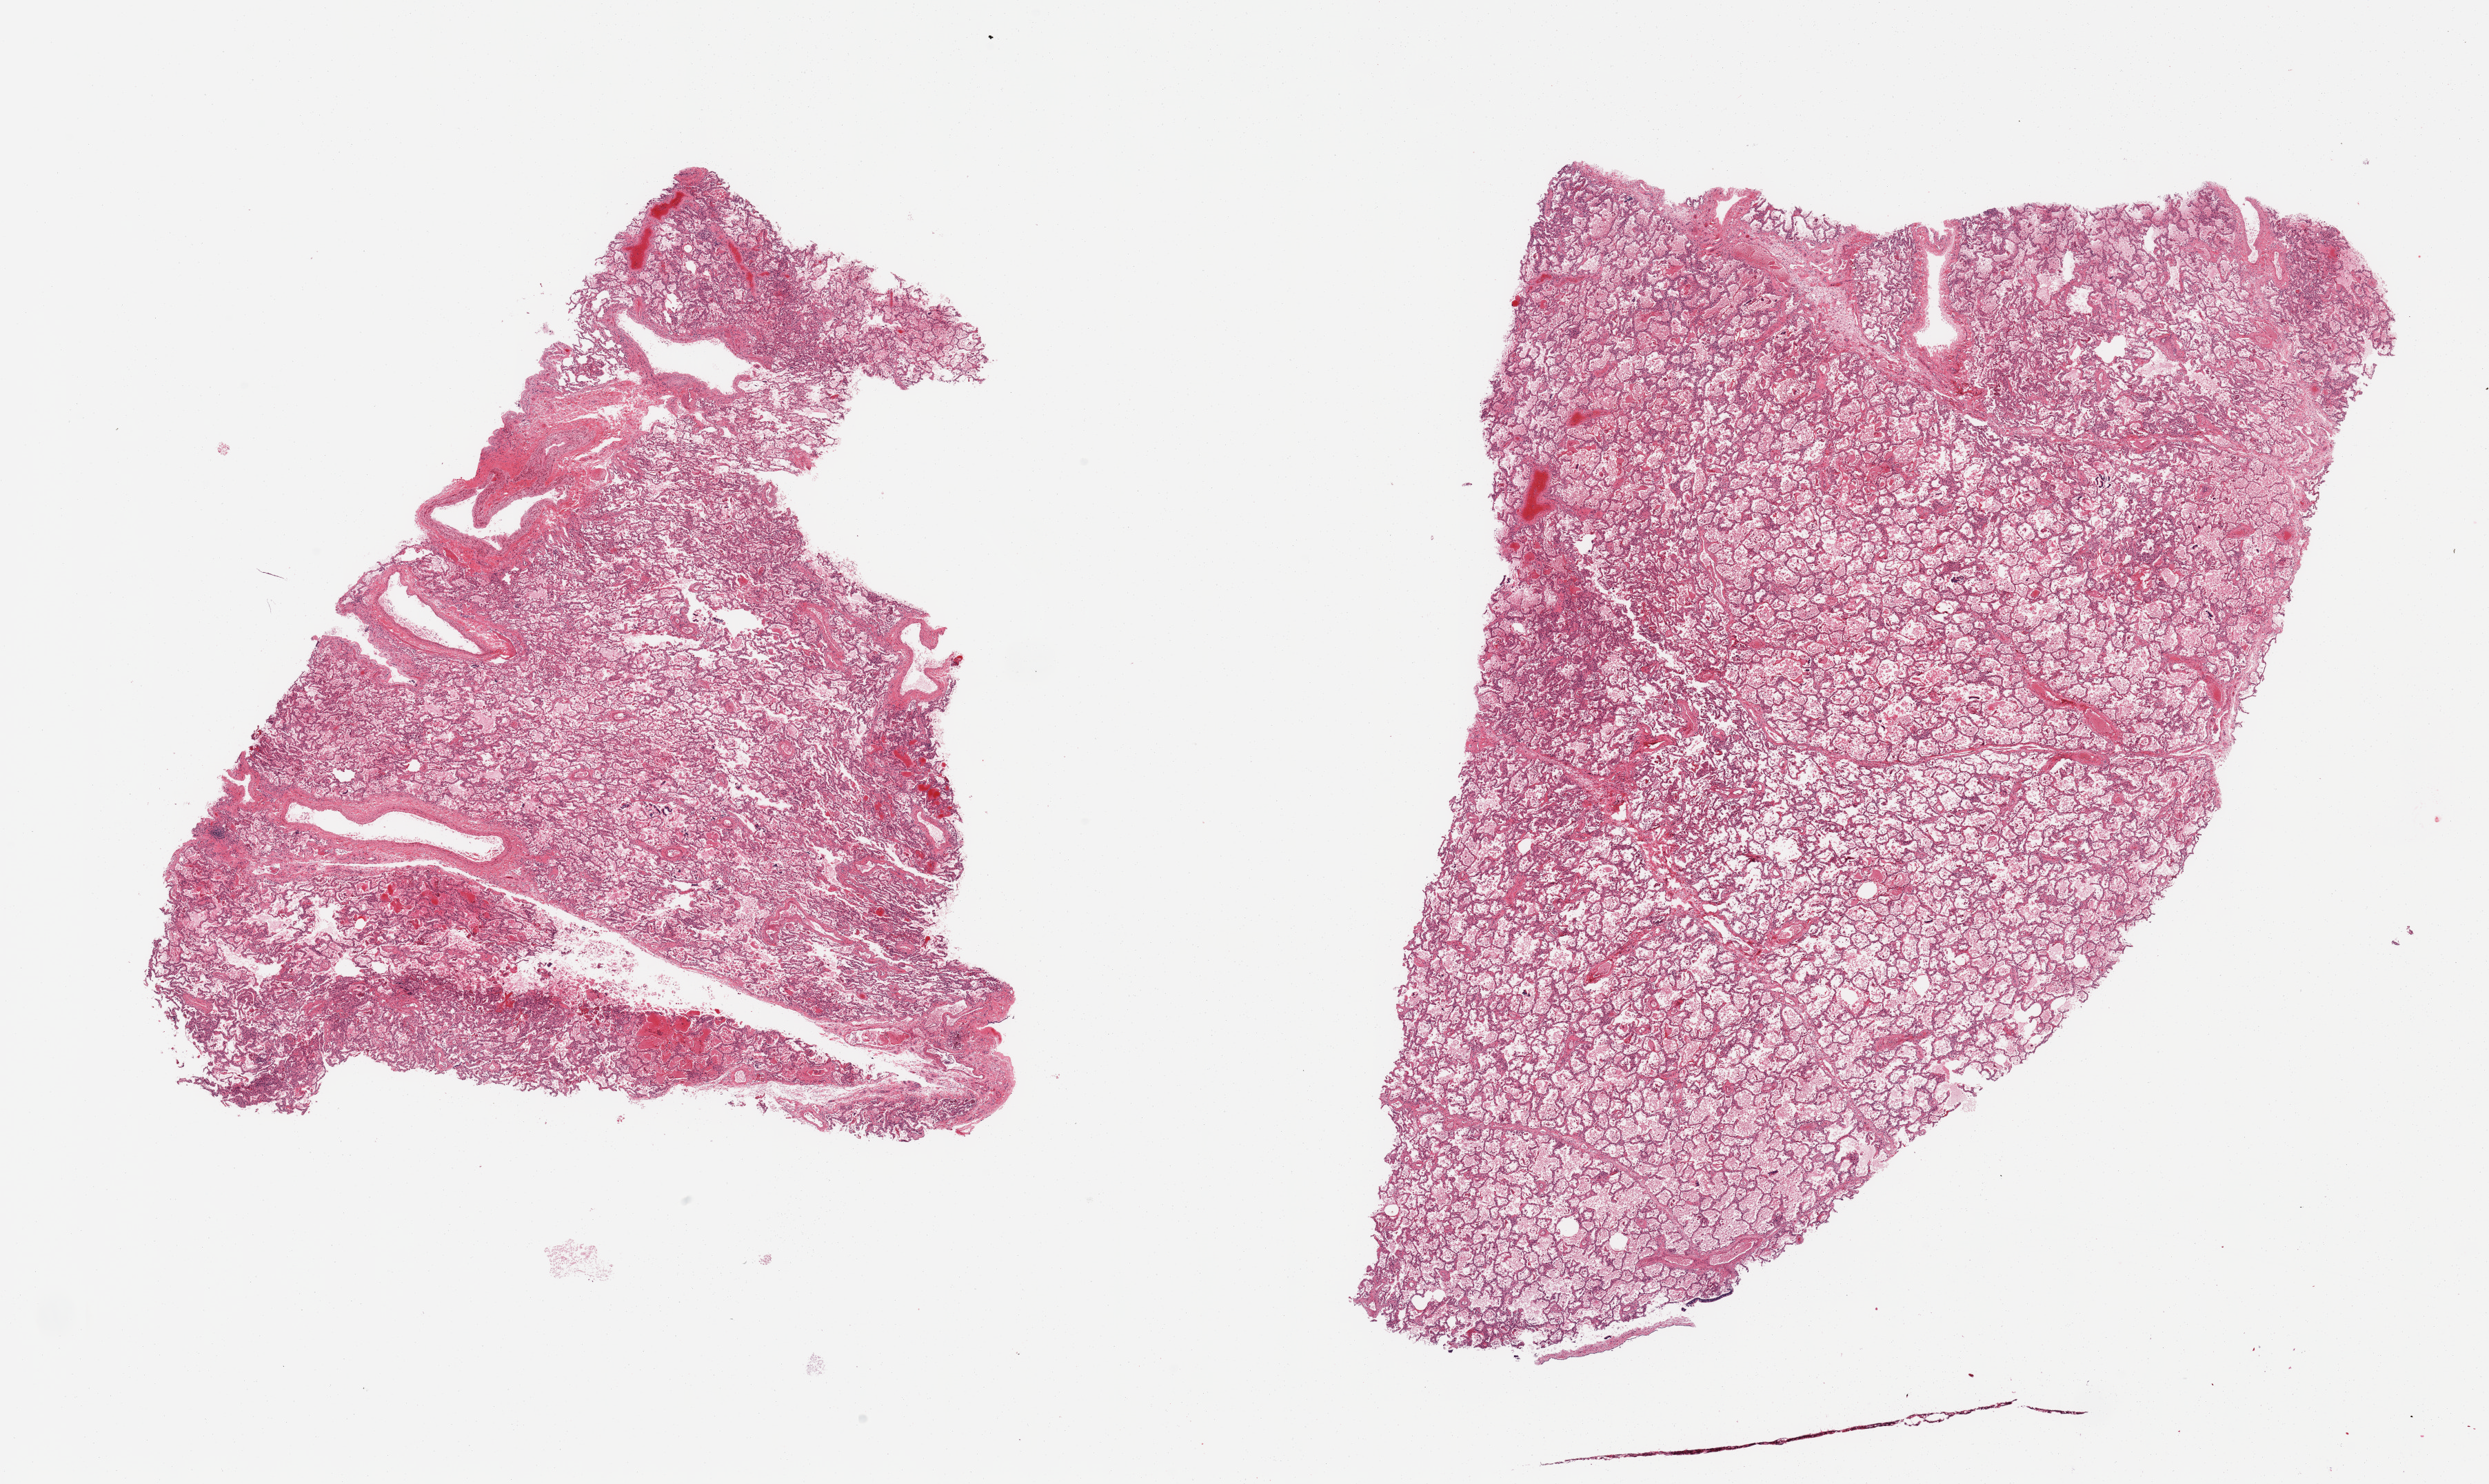
H&E whole-slide image, shown as a low-resolution overview of the whole scanned area (about 28.5 x 17.0 mm), PAXgene-fixed paraffin-embedded (PFPE) section, section of lung (target tissue), donor tissue sample. Donor: female.
Review note (as recorded): 2 pieces; alveolar edema & hemorrhage; delicate well preserved infrastructure.